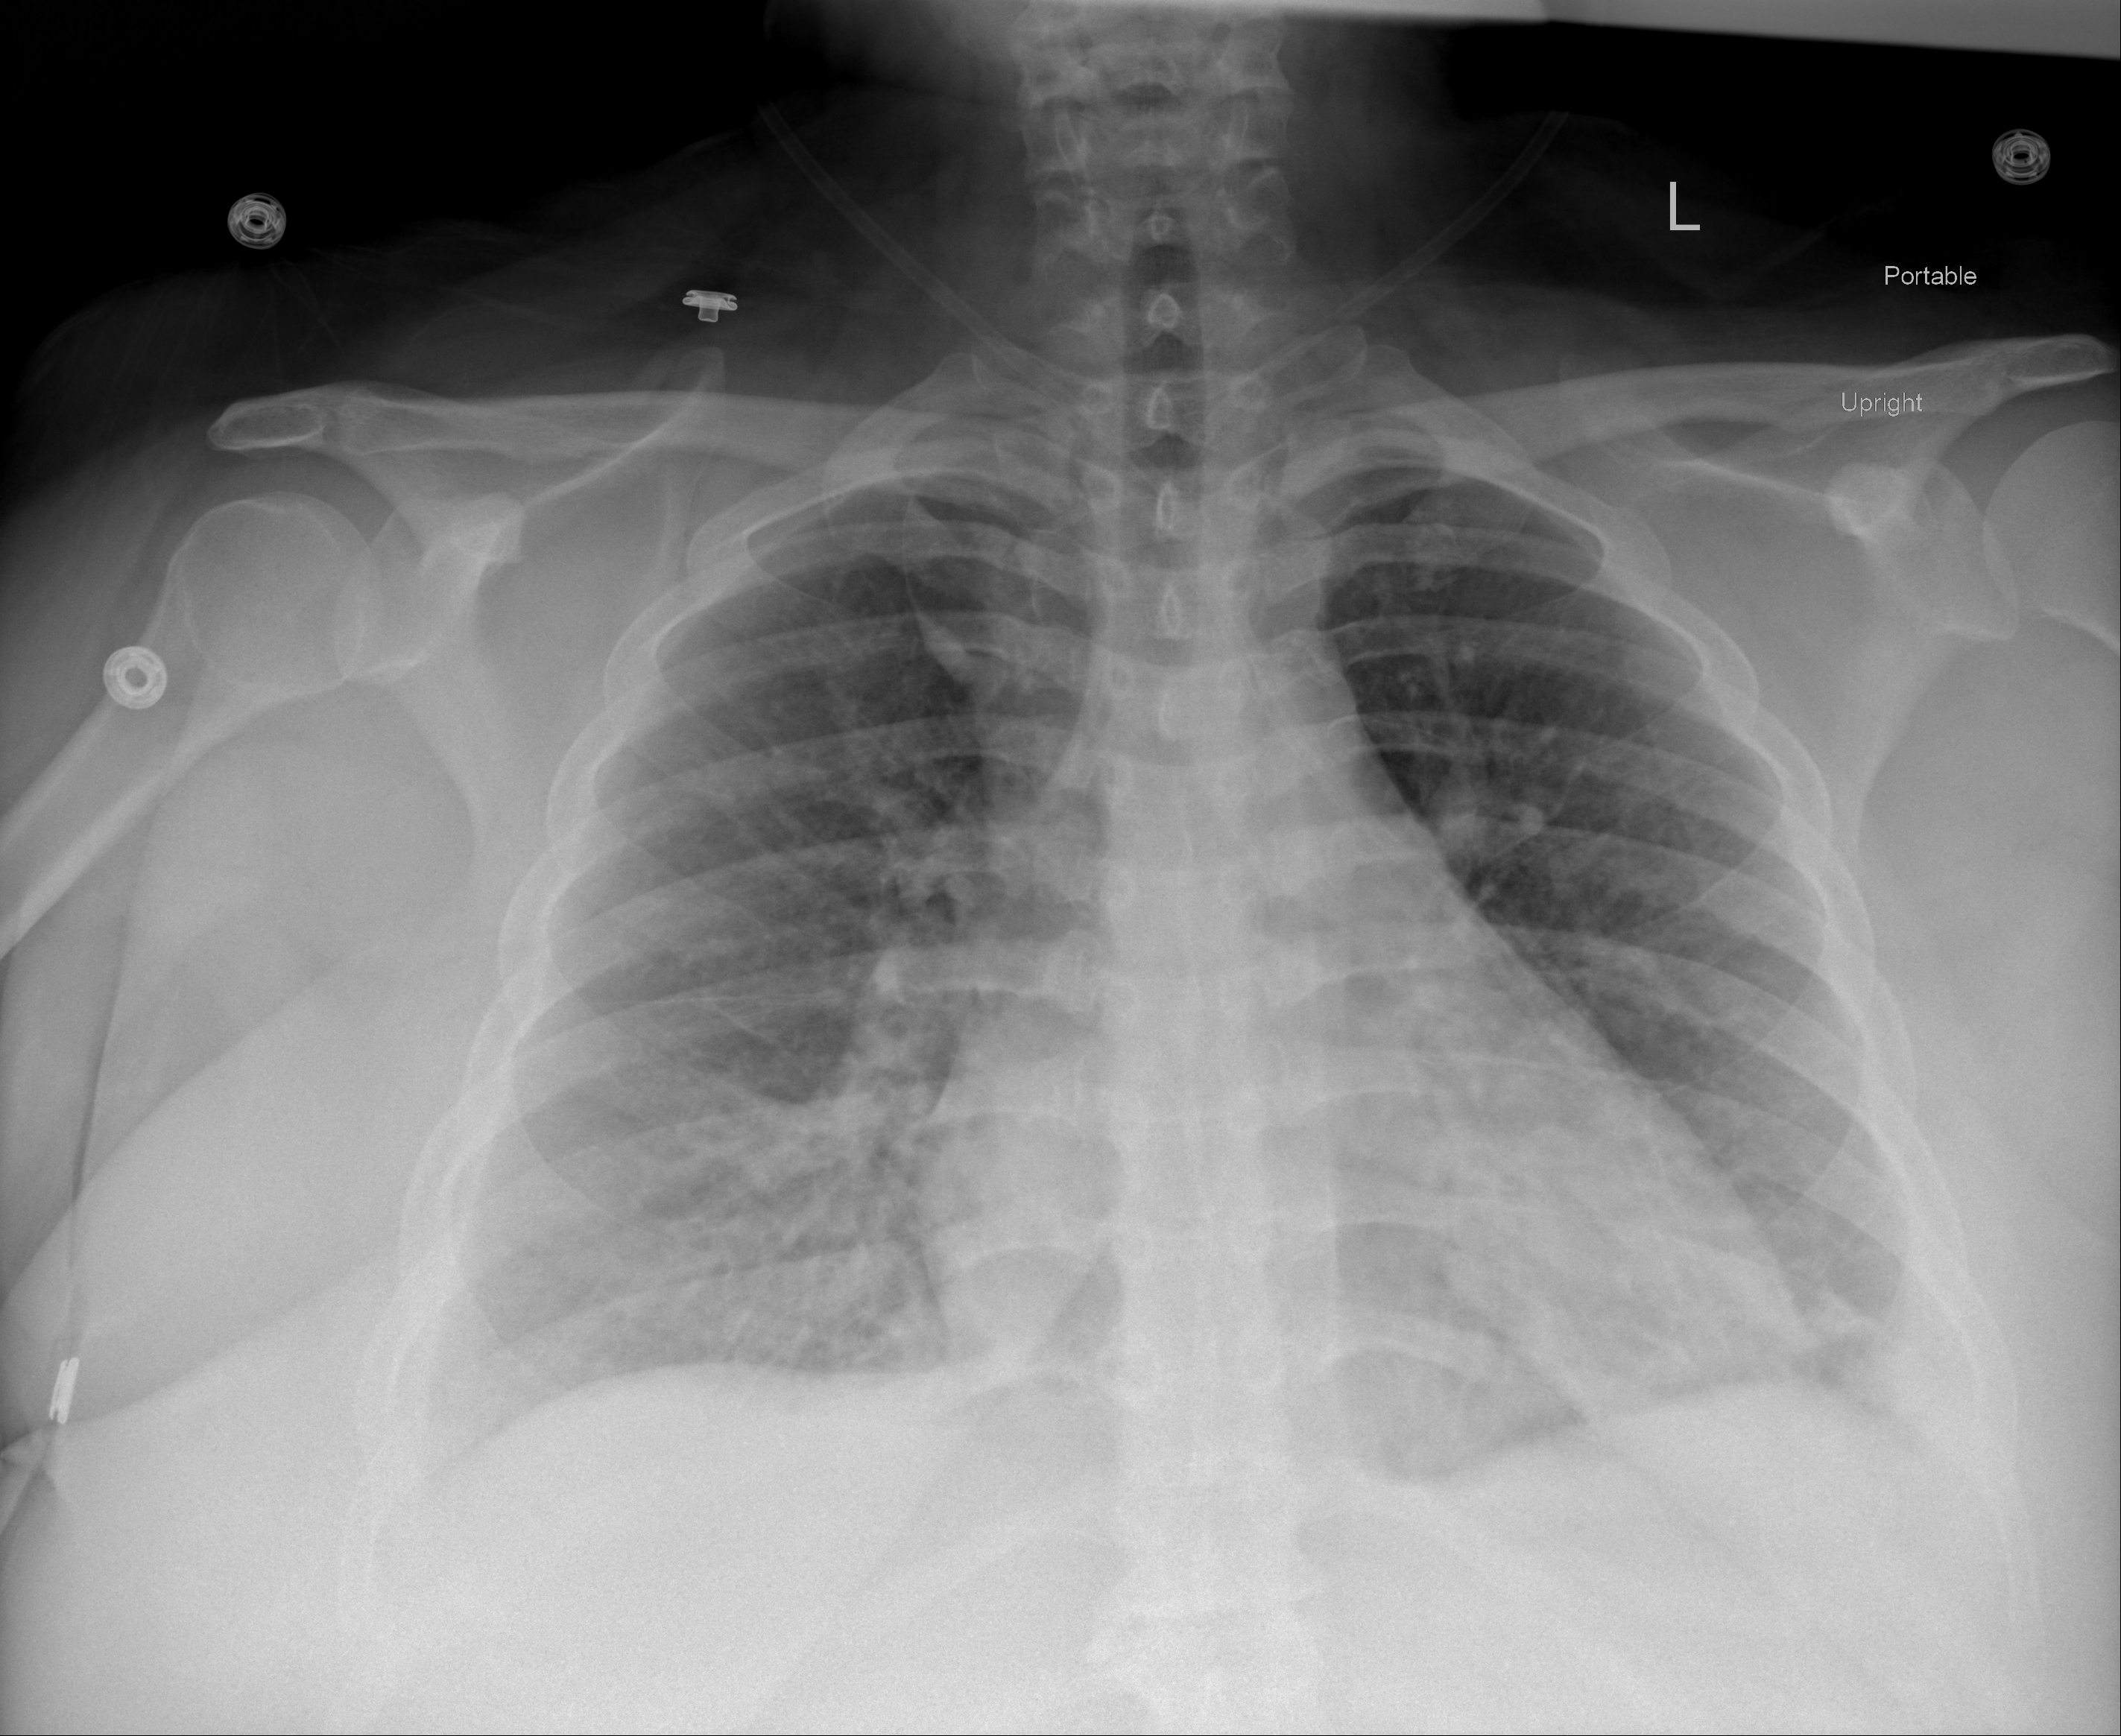
Chest X-ray (portable), AP projection. Female patient, age 37 years; COVID-19 (test-positive).
Radiologist key findings (as recorded): Subtle bibasilar opacities are noted.